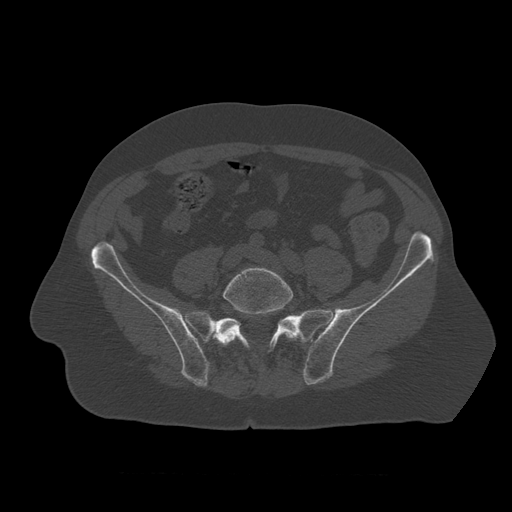
CT including the spine, one axial slice; position 246 of 450 along the scan axis; reconstruction kernel STANDARD; 120 kVp; bone window (W 1800 / L 400 HU); 512 × 512 image matrix, field of view 405 × 405 mm. Patient age 75 years. From the clinical record (not read from this slice): primary cancer: prostate.
Structures marked on this image (semi-automatically segmented with operator editing):
- L5 vertebra: box from (x=219, y=267) to (x=297, y=347) px